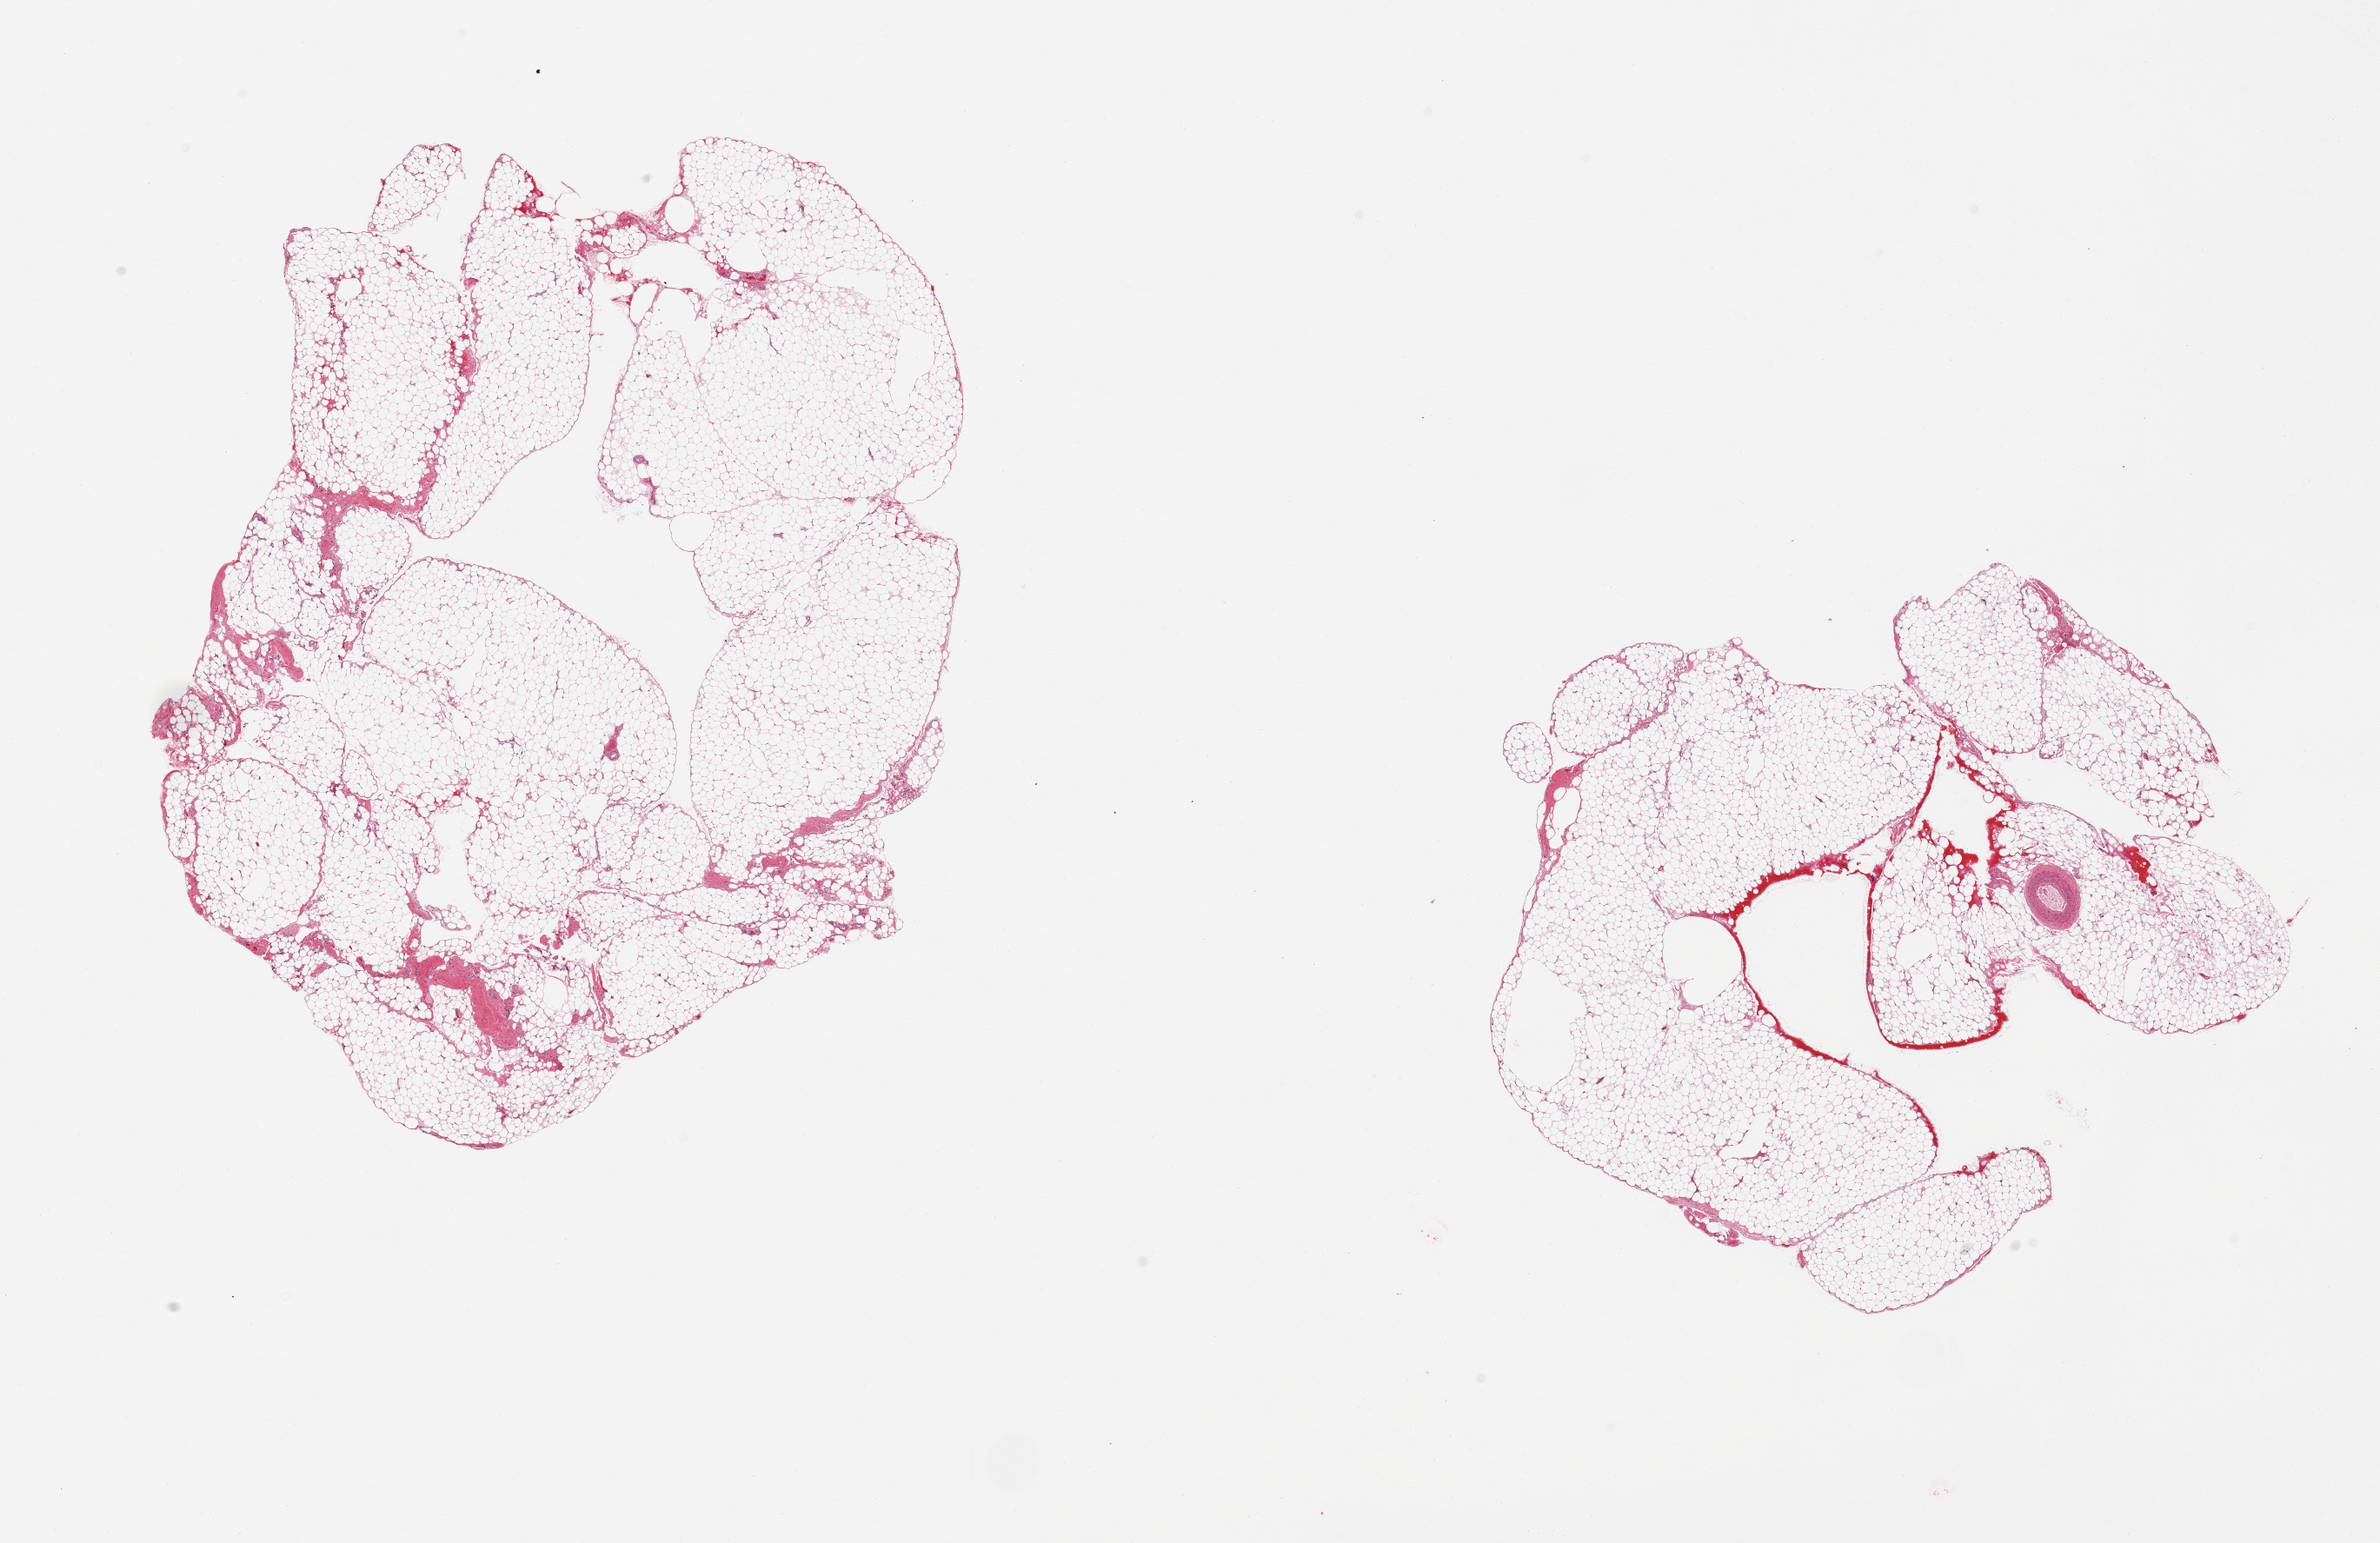
Digitized haematoxylin and eosin-stained section, low-resolution overview of the scanned area, about 21.7 x 14.0 mm (from a 20x scan). PAXgene-fixed, paraffin-embedded tissue. Sampled site (target tissue): omentum. Tissue donor sample.
Reviewer comment on this tissue sample: 2 pieces, ~5-10% fascia.